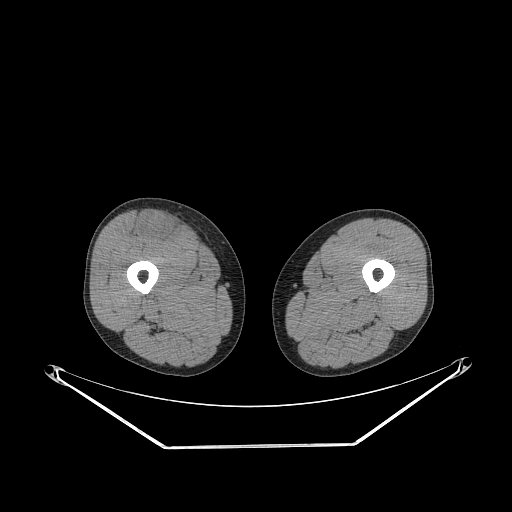
CT of an extremity soft-tissue mass (from a PET/CT study), one axial slice. Slice 254 of 311 in the series (ordered by position). Reconstruction kernel STANDARD. Soft-tissue window (W 400 / L 40 HU). 3.75 mm slice thickness. 512 × 512 image matrix. Male patient. From the clinical record (not read from this slice): histological type: pleiomorphic leiomyosarcoma; grade: intermediate; site of the primary tumour: right thigh.
Annotated regions visible in this slice (expert contour drawn on MRI and transferred to this co-registered scan by the dataset authors):
- gross tumour volume including surrounding oedema: bounding box <139,212,179,241> (left, top, right, bottom; pixels)